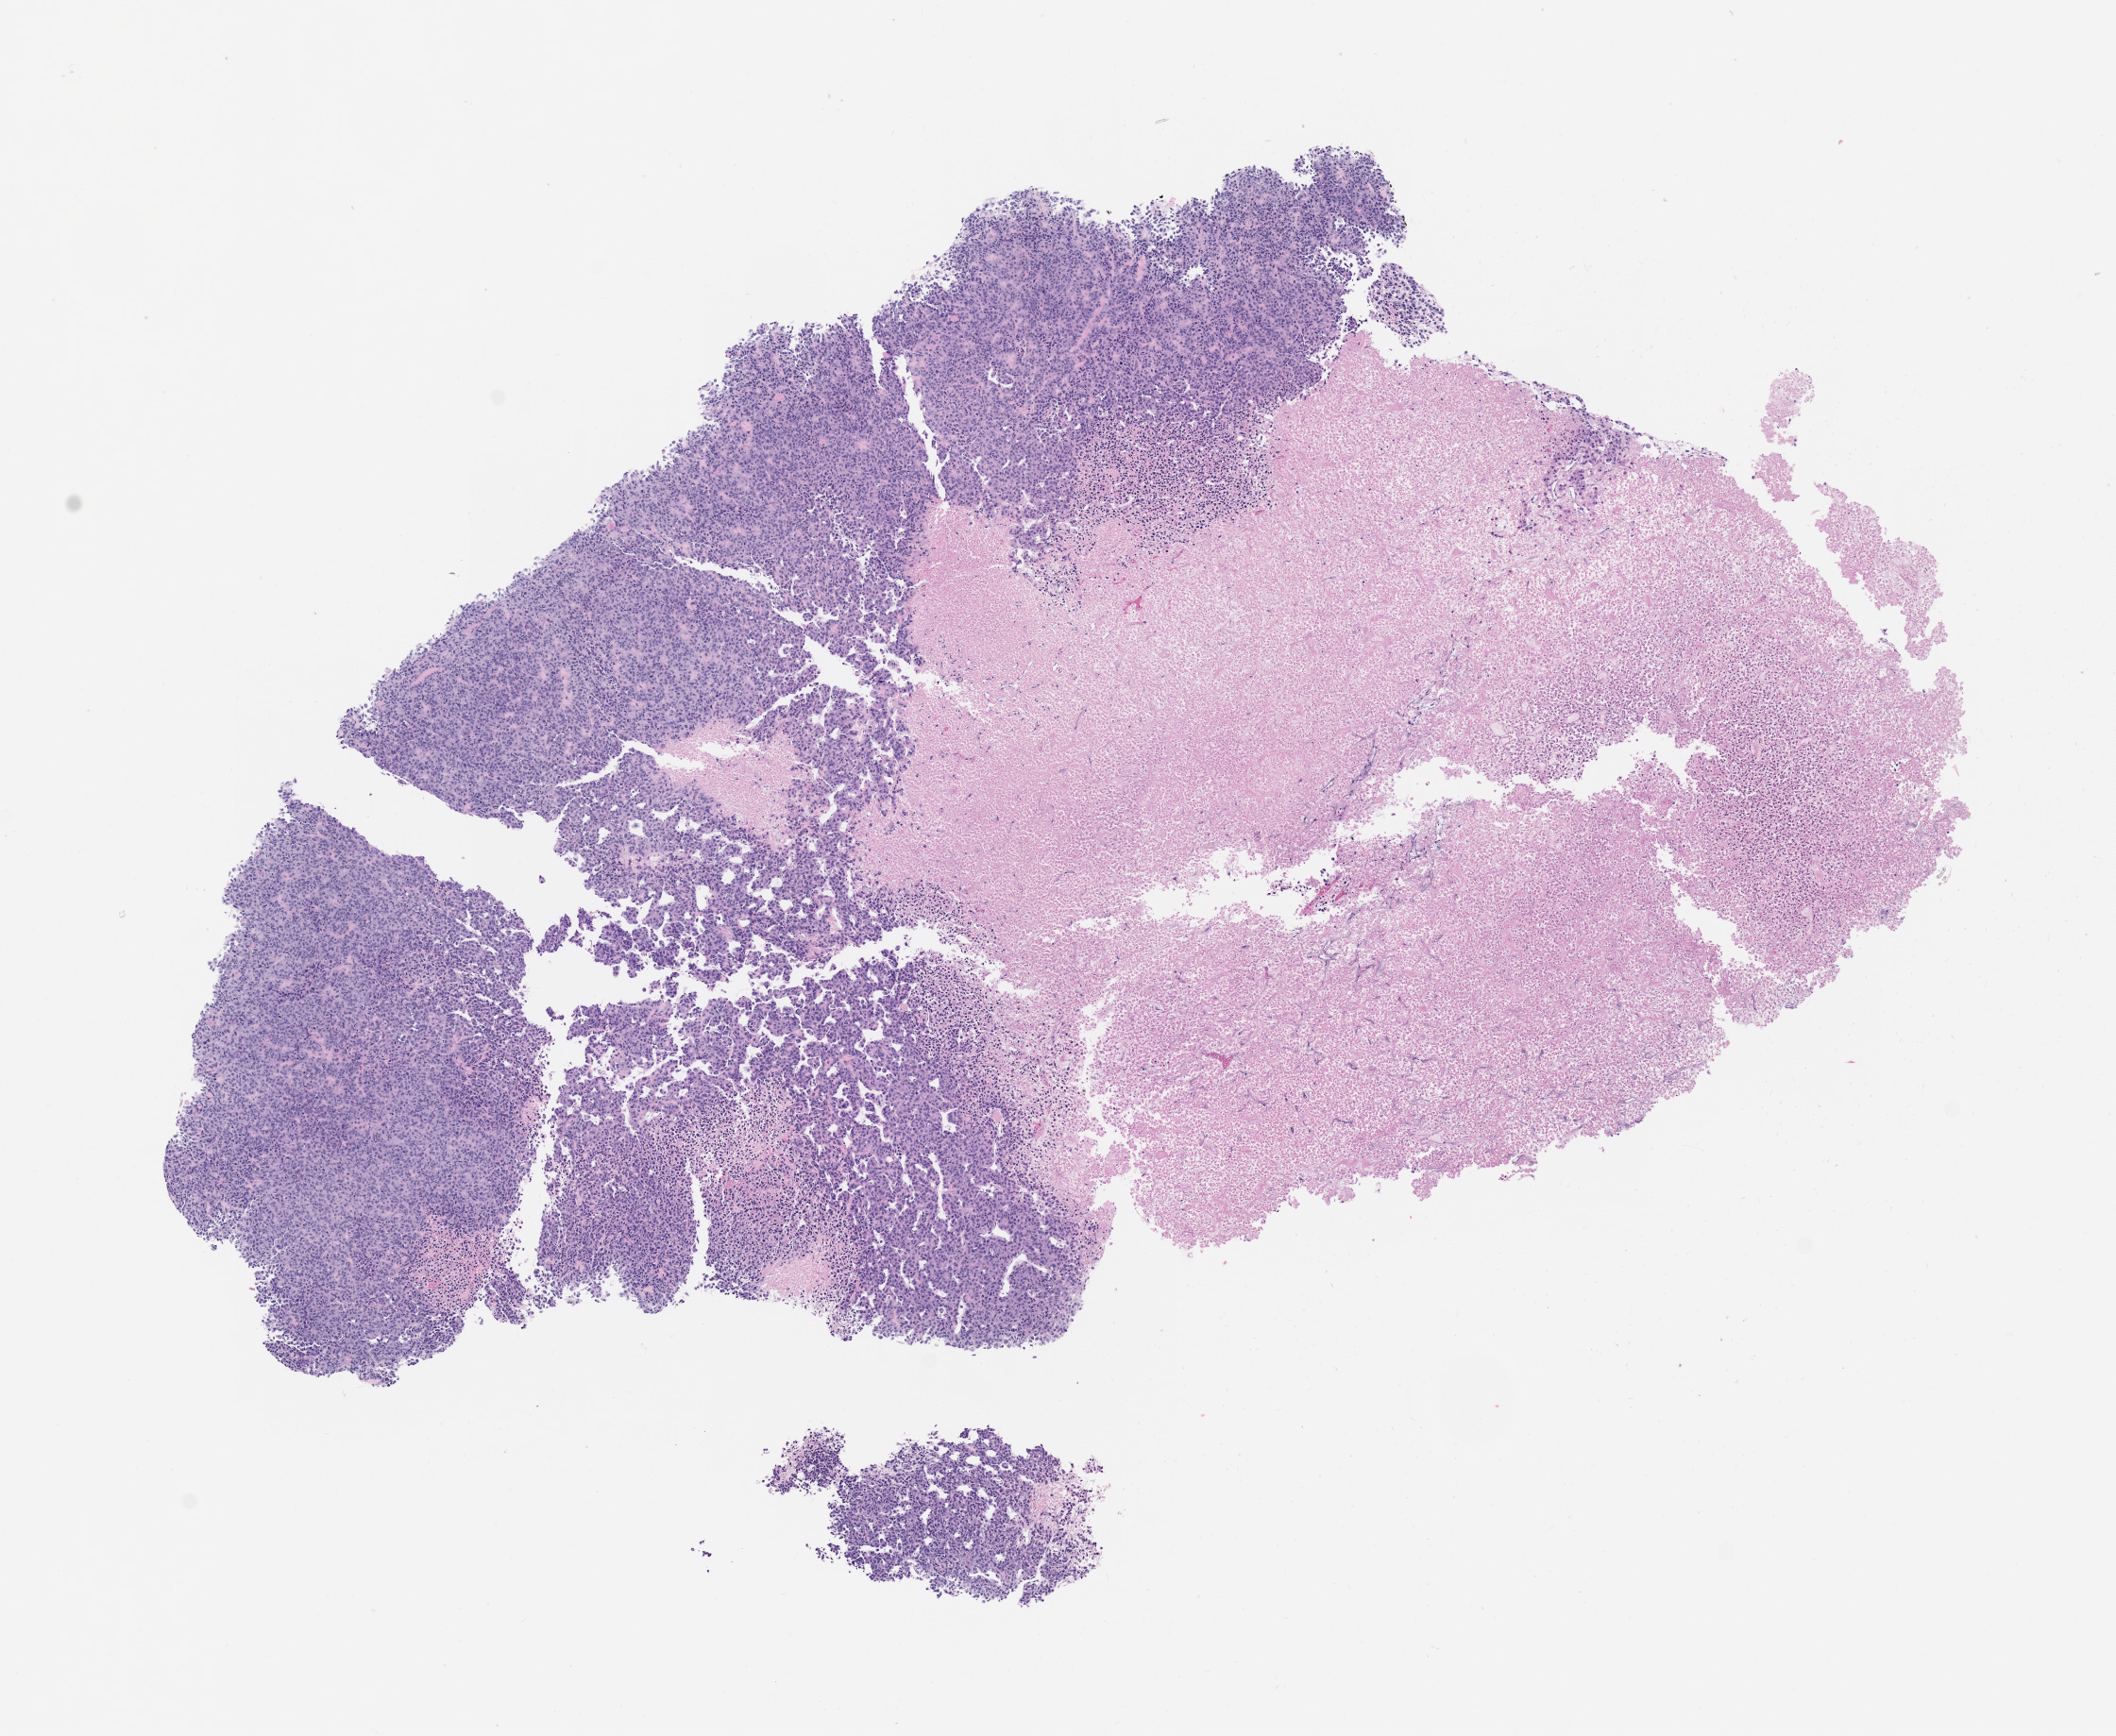
Hematoxylin and eosin (H&E) whole-slide image of a patient-derived xenograft (PDX) tumor grown in a mouse, passage 1 — whole scanned area (about 9.0 x 7.4 mm) shown as a low-resolution overview; formalin-fixed, paraffin-embedded (FFPE) tissue; tumor site category: bone.
• originating patient diagnosis: Osteosarcoma